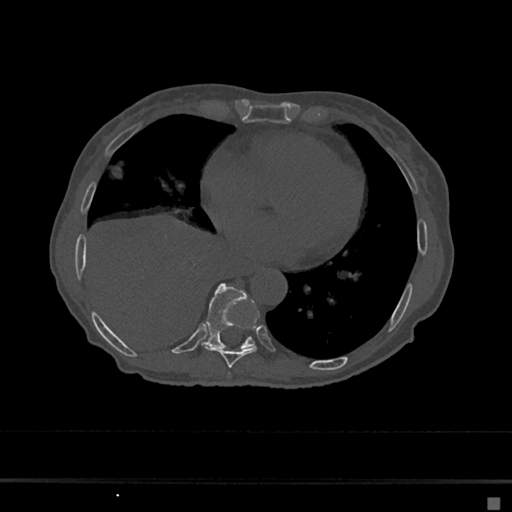
CT including the spine, one axial slice; position 301 of 797 along the scan axis; bone window (W 1800 / L 400 HU); 0.5 mm slice thickness; 512 × 512 image matrix. Female patient, age 68 years. Case-level facts recorded for this patient, not image findings: primary cancer: renal.
Annotated regions visible in this slice (semi-automatic segmentation, software-assisted and operator-edited):
- T7 vertebra: box from (x=228, y=373) to (x=230, y=375) px
- T8 vertebra: (x=205, y=316)–(x=258, y=368)
- T9 vertebra: (x=204, y=283)–(x=255, y=349)